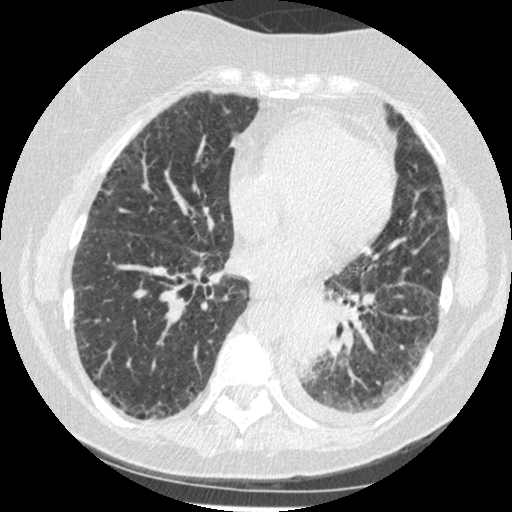
Low-dose screening chest CT, one axial slice; position 91 of 341 along the scan axis; 120 kVp; lung window (W 1500 / L -600 HU); 1.25 mm slice thickness; 512 × 512 image matrix, field of view 310 × 310 mm.
Structures marked on this image (manually delineated by an expert):
- lesion 1 (tumor, lower lobe of left lung): bounding box <289,313,328,369> (left, top, right, bottom; pixels)